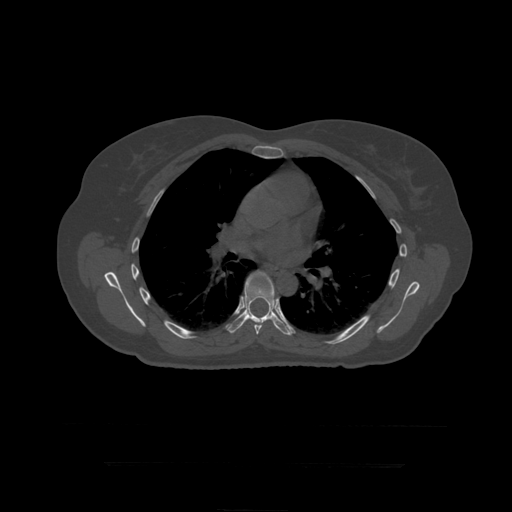
CT including the spine, one axial slice; position 290 of 399 along the scan axis; 120 kVp; bone window (W 1800 / L 400 HU); 512 × 512 image matrix, field of view 450 × 450 mm. Patient age 41 years. Case-level facts recorded for this patient, not image findings: primary cancer: breast.
Annotated regions visible in this slice (semi-automatically segmented with operator editing):
- T7 vertebra: bounding box <245,271,275,335> (left, top, right, bottom; pixels)
- T8 vertebra: <227,272,291,336>